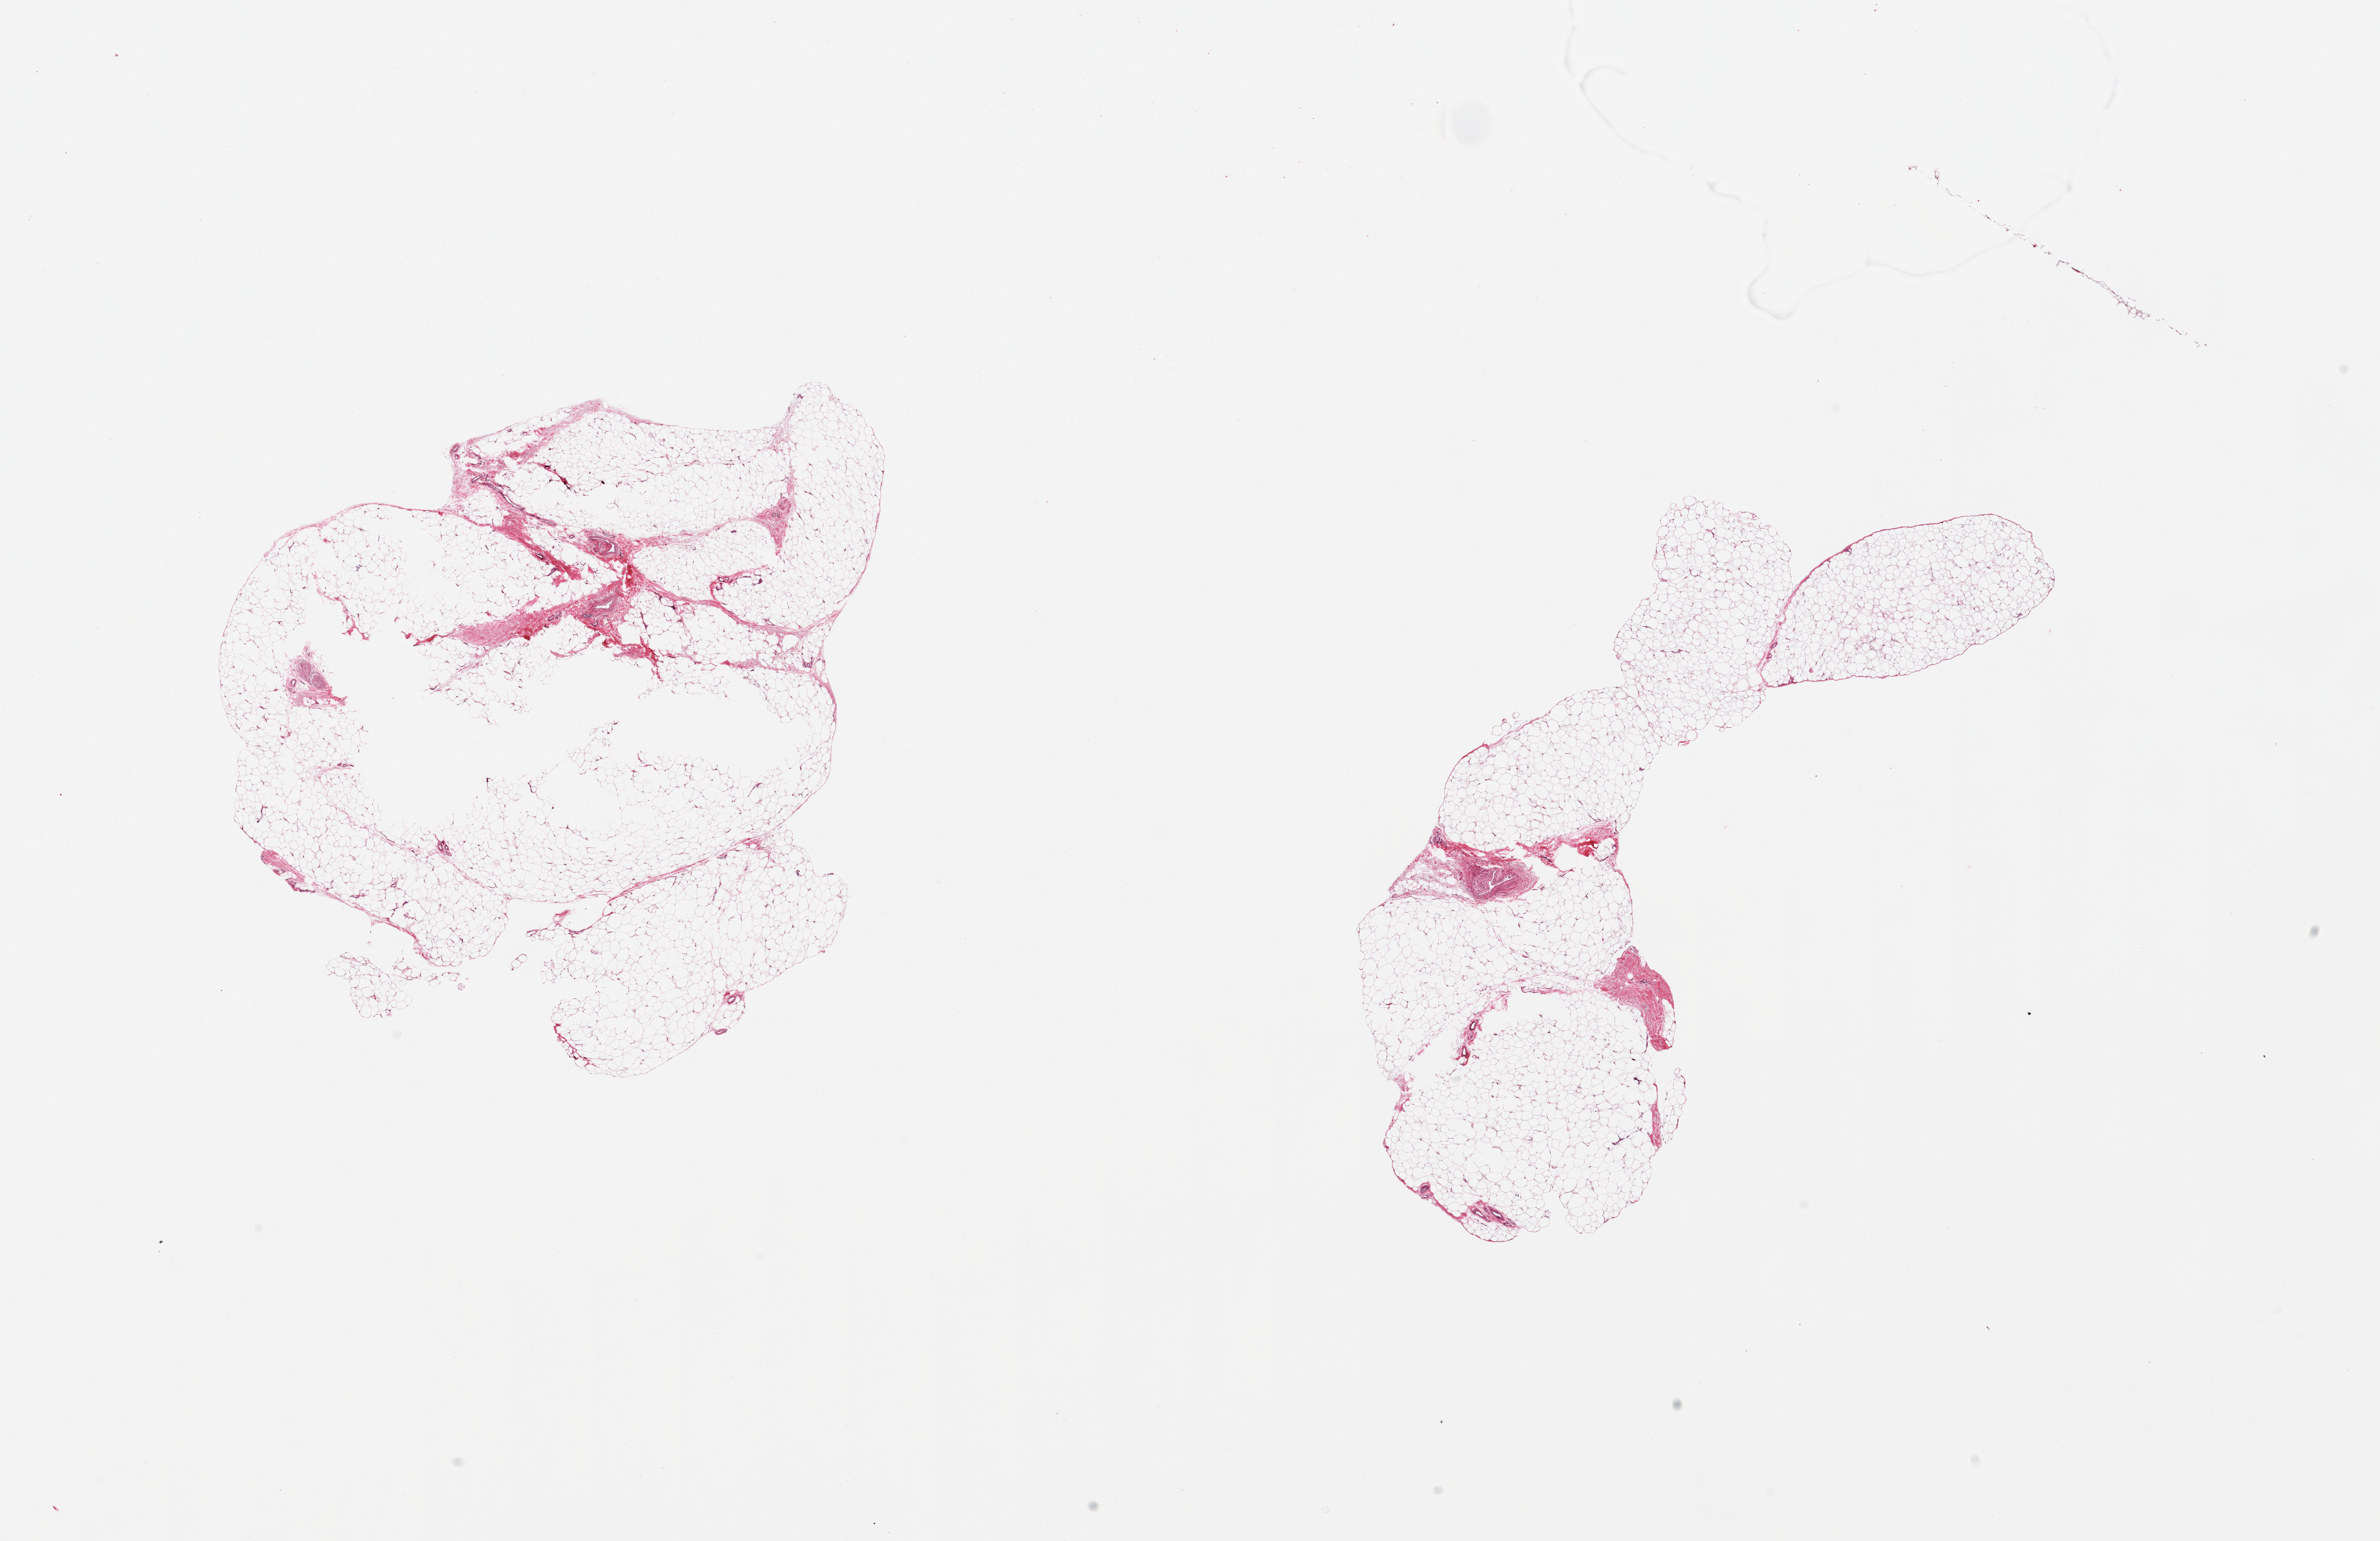
Digitized H&E-stained section, brightfield — a low-resolution overview of the entire scanned area, about 27.6 x 17.9 mm (from a 20x scan). PAXgene-fixed, paraffin-embedded tissue. Sampled site (target tissue): adipose tissue. Tissue donor sample. Donor: female.
Pathologist's review note for this sample: 2 pieces, ~10% fascia,vascular elements.